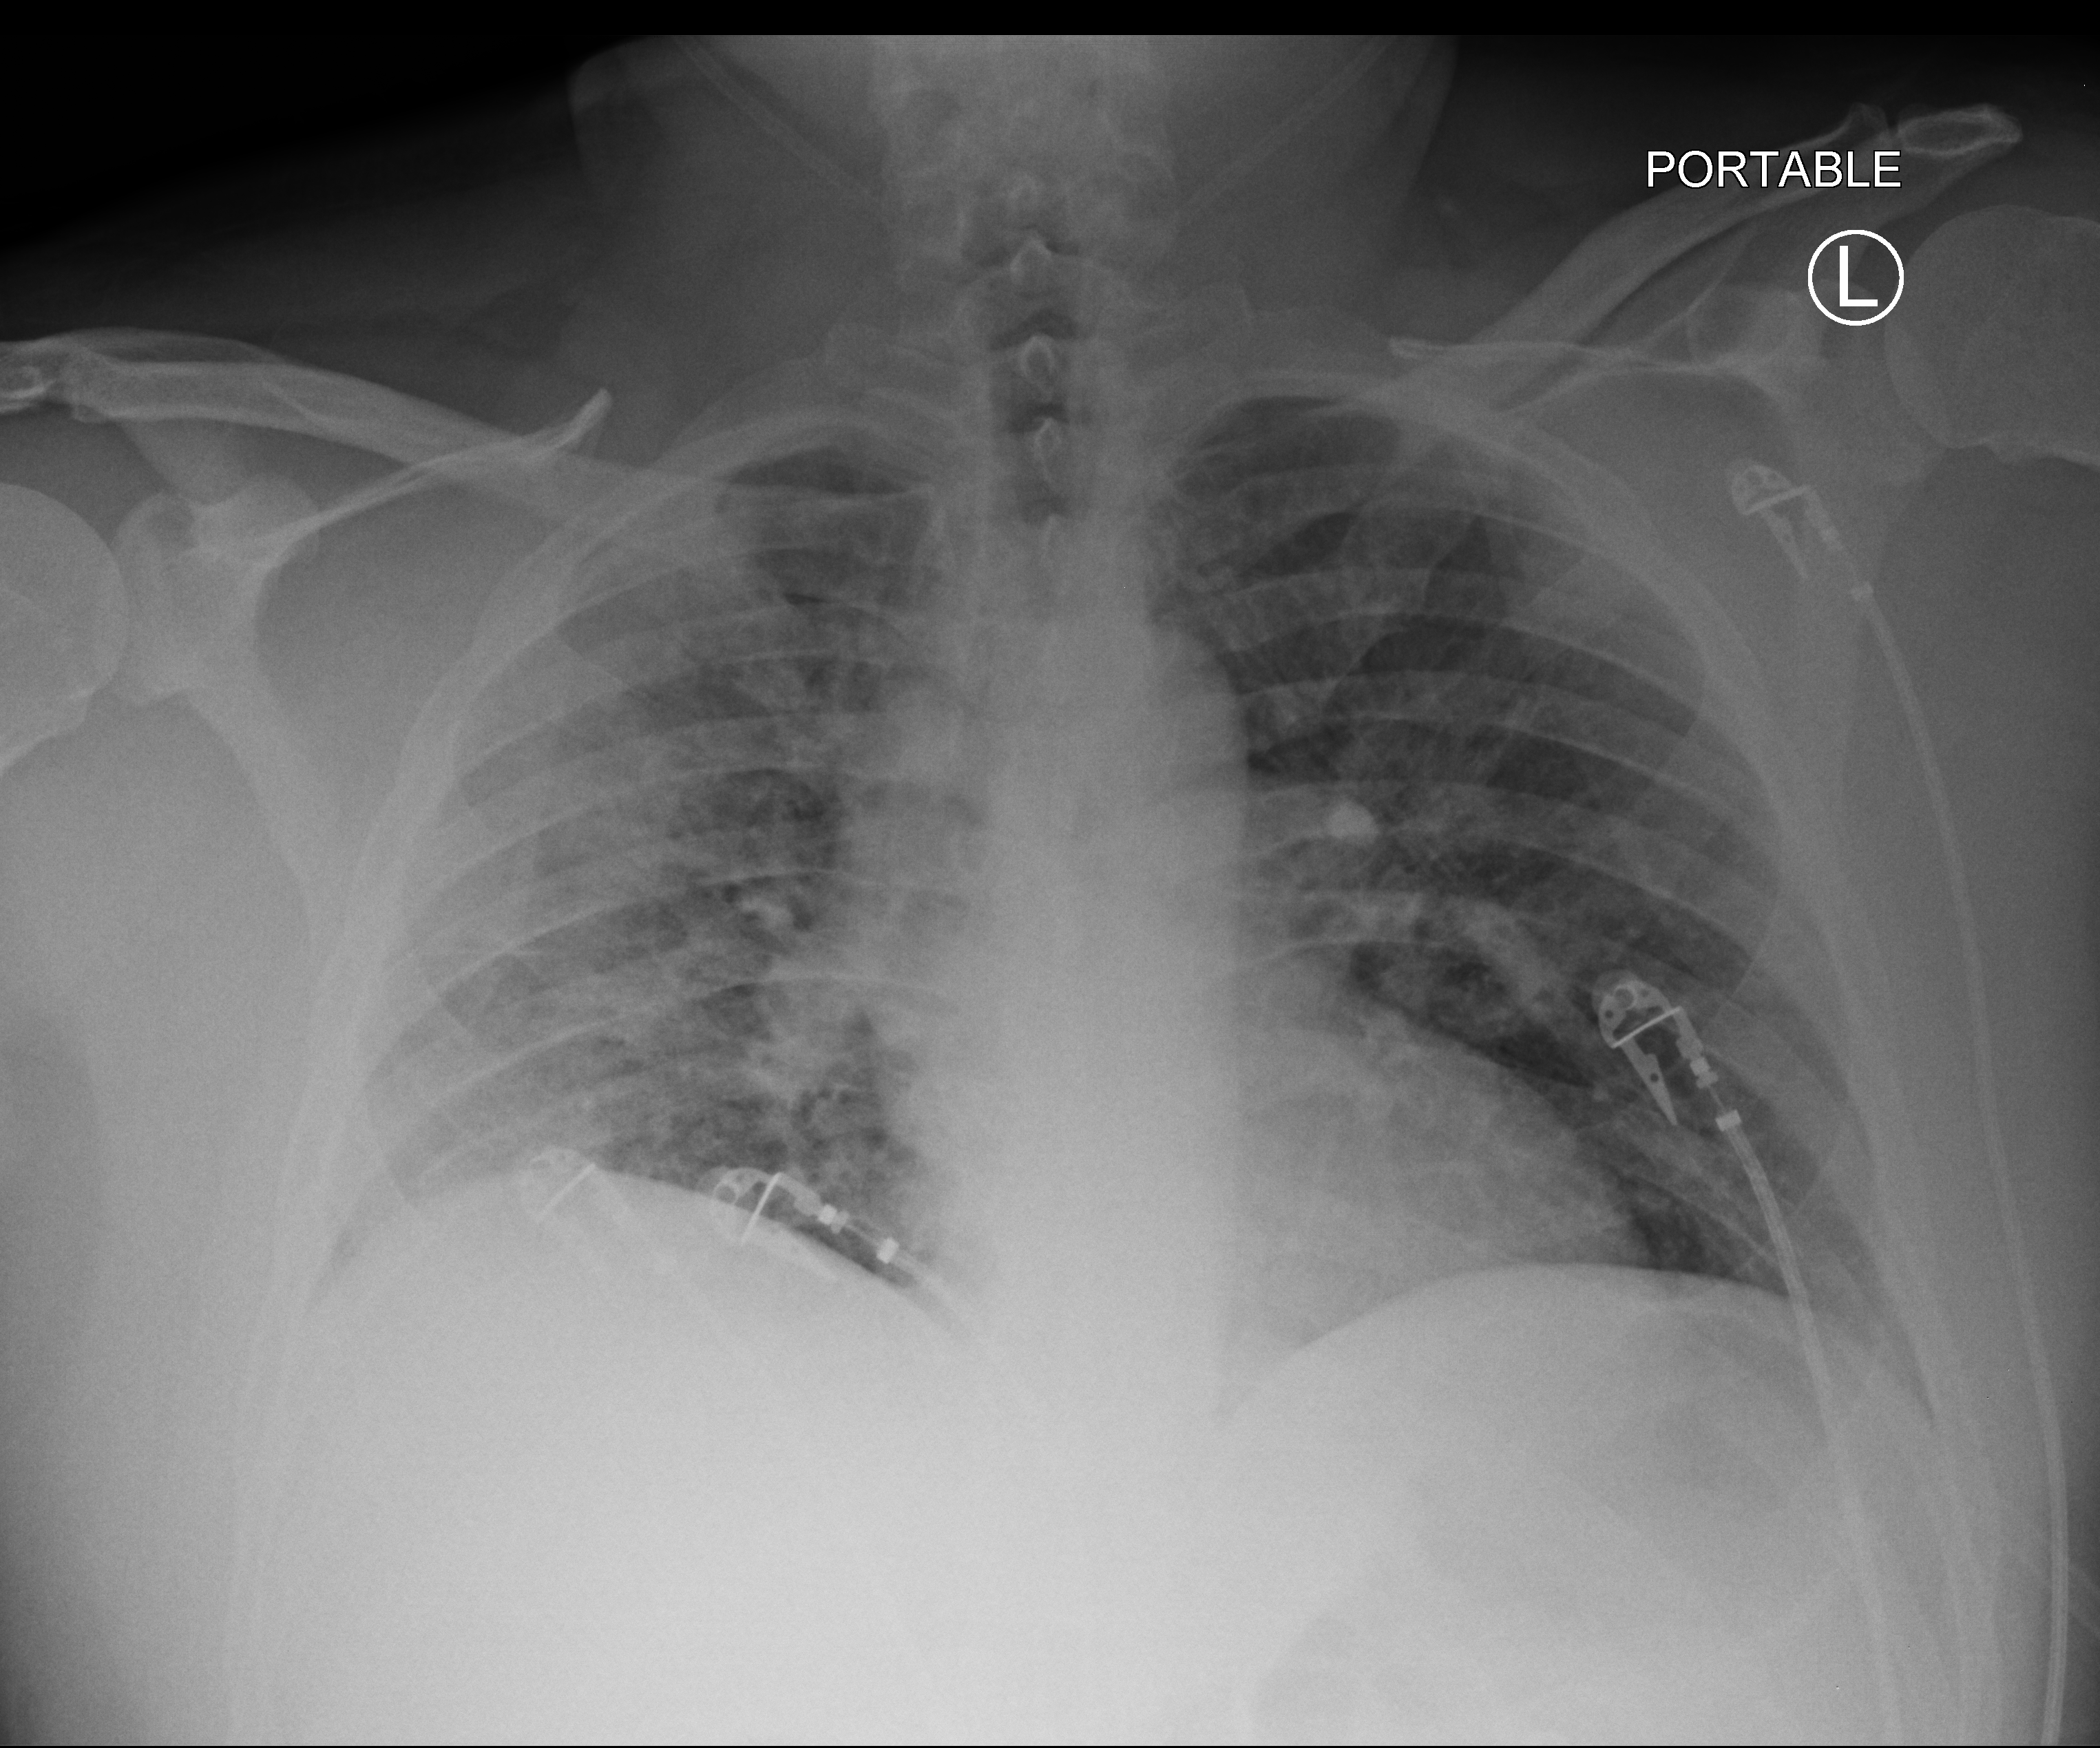
Portable chest radiograph; anteroposterior (AP) projection. Patient hospitalised with COVID-19; male, aged 18–59 years.
From the hospital-stay record, not from the radiograph (when in the stay this image was taken is not recorded): mechanically ventilated during this hospital stay: yes.